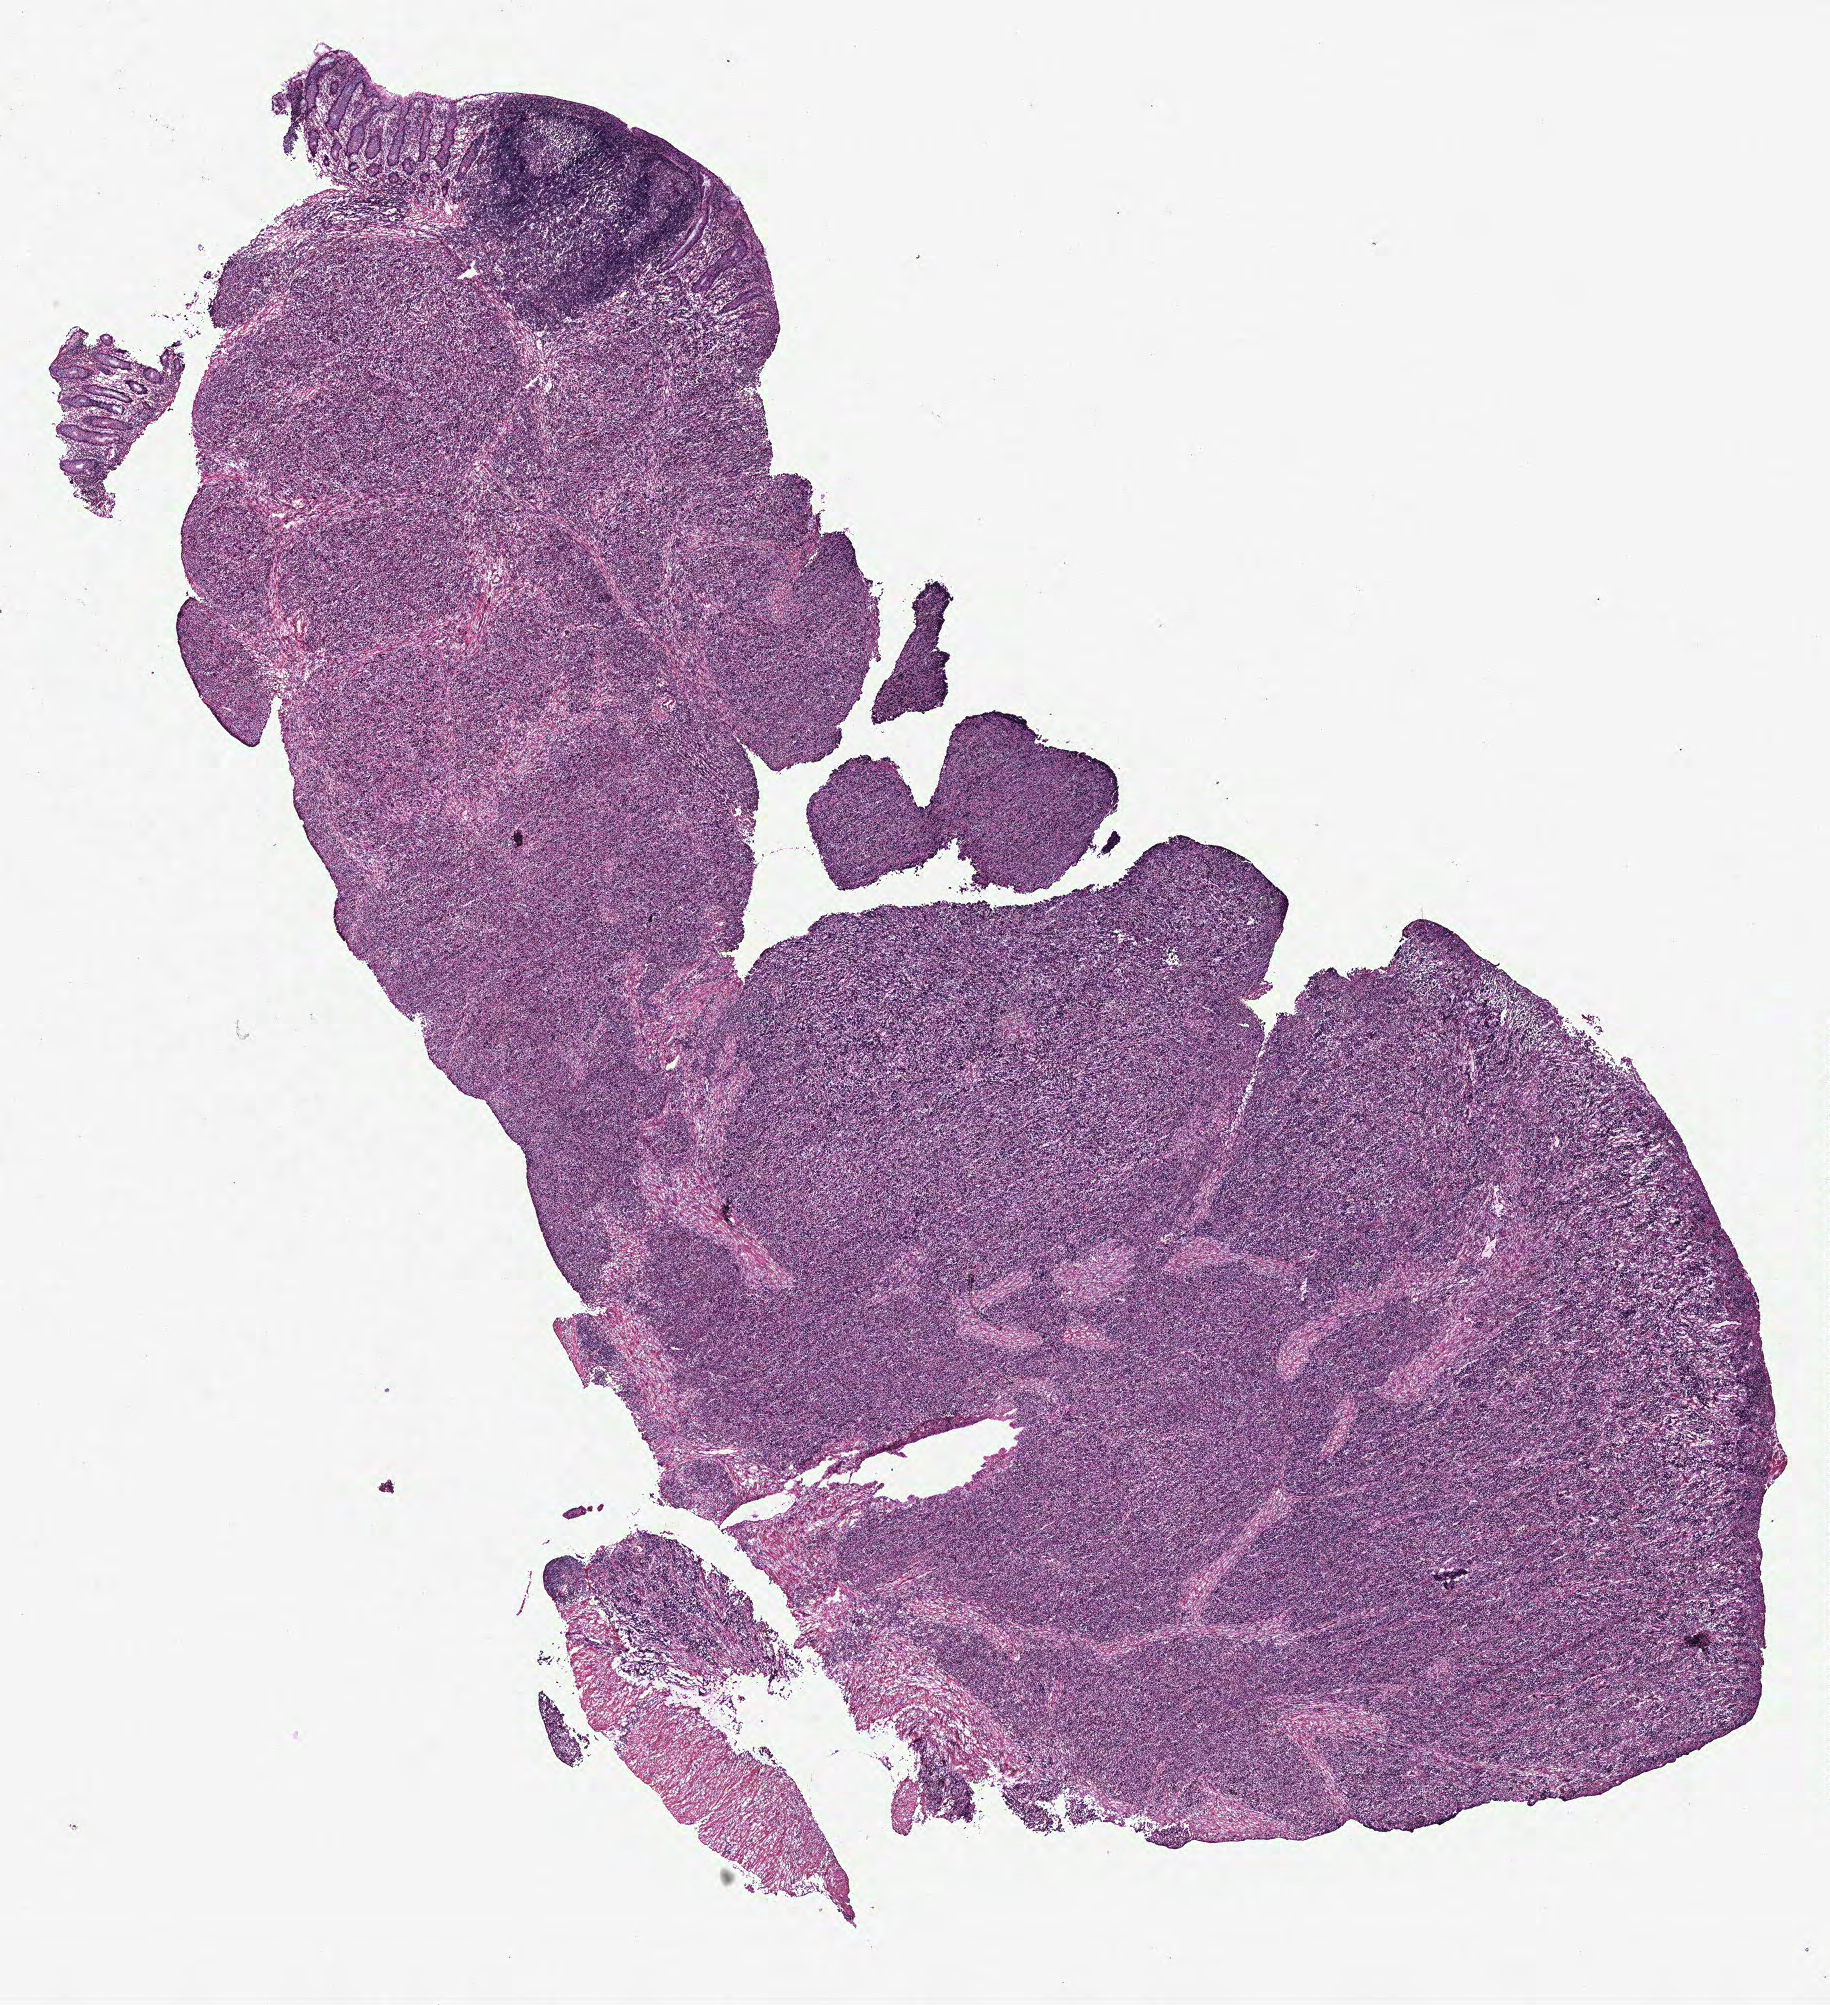
H&E-stained whole-slide image — low-resolution overview of the scanned area, about 14.6 x 16.0 mm (from a 40x scan). Colon, tissue type not recorded.
Patient diagnosis (cohort enrolment): colon cancer (colon).